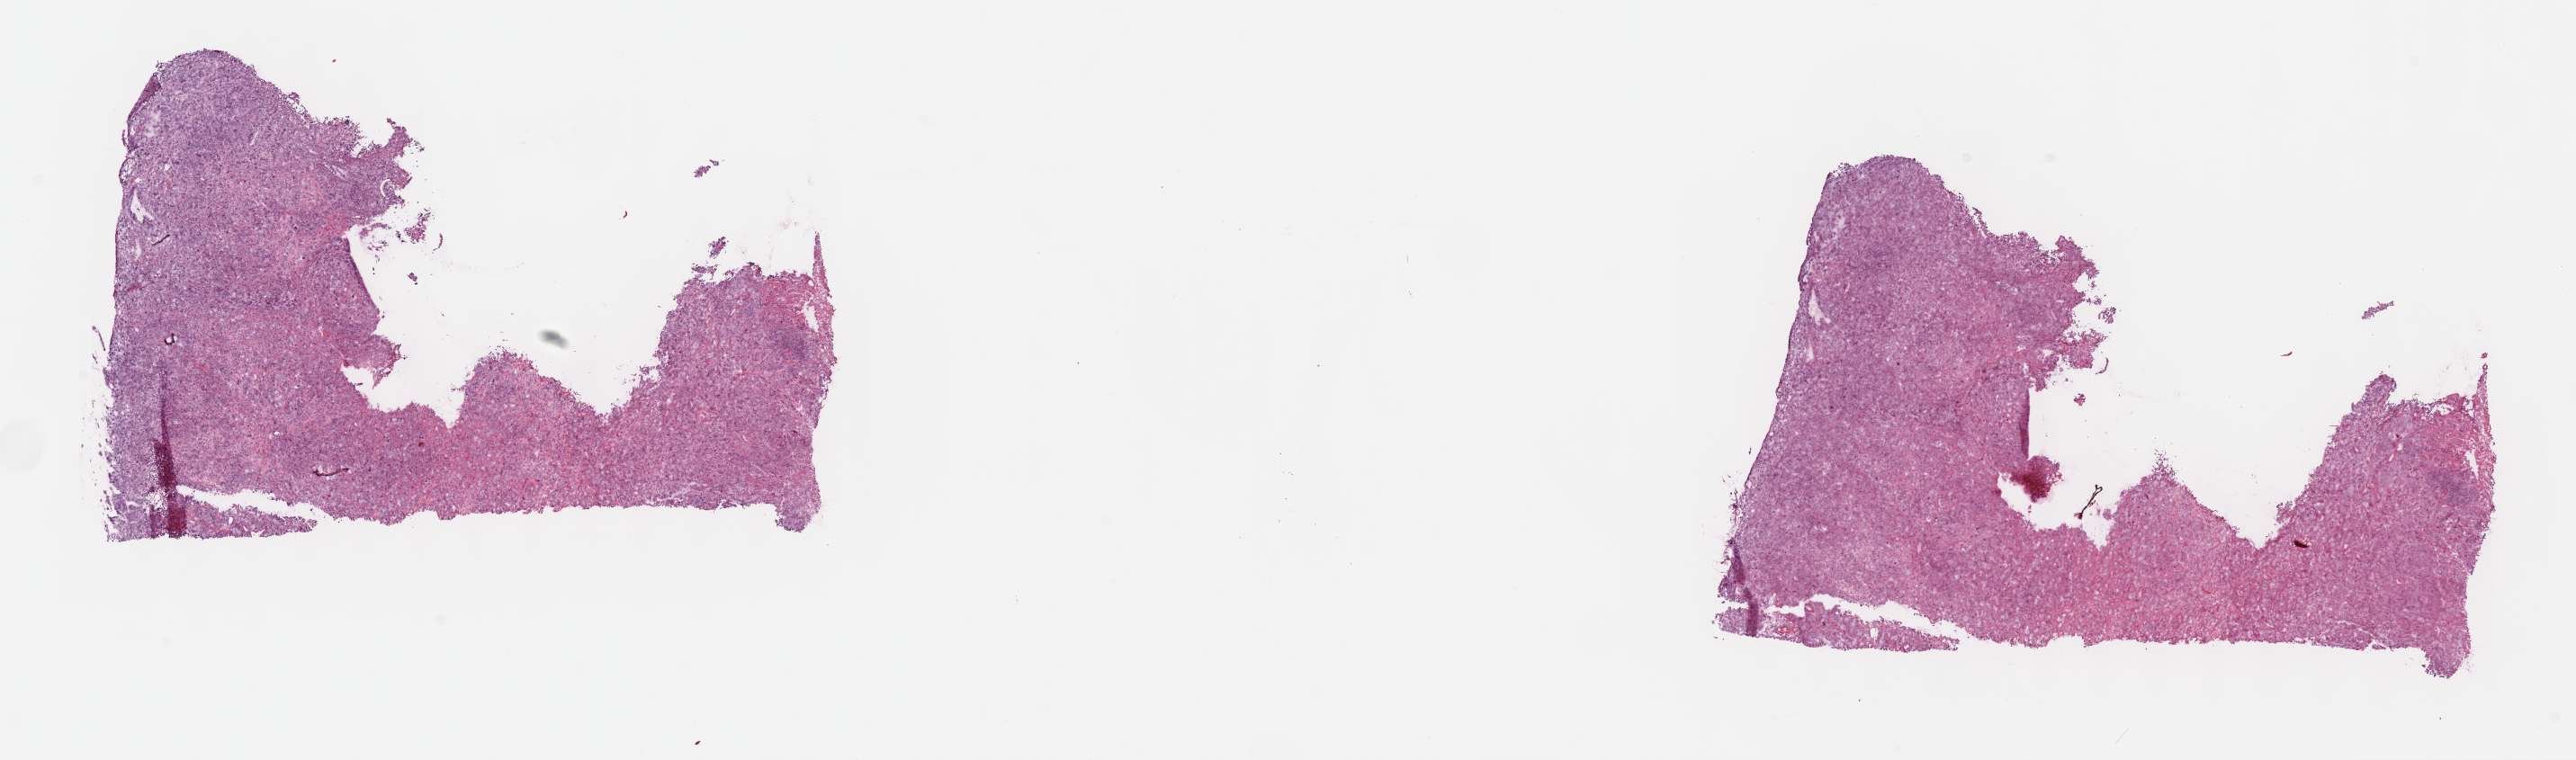
Whole-slide histology image, H&E, whole scanned area (about 23.2 x 6.8 mm) shown as a low-resolution overview, frozen section from the top of the tissue portion, sample: primary tumour, stomach. Female patient; age at initial diagnosis 73 years. Histologic grade: G3 (poorly differentiated). Pathologist review of this section (percent, as recorded): tumour cells 70%, tumour nuclei 70%, normal cells 0%, stromal cells 20%, necrosis 10%. Inflammatory infiltration, as recorded: lymphocyte infiltration 40%, monocyte infiltration 20%, neutrophil infiltration 20%.
Lymph nodes positive (case pathology): 1 of 35 examined. Histologic diagnosis: Adenocarcinoma, NOS (cardia, NOS). TNM: T3 N1 M0. AJCC pathologic stage: IIB.